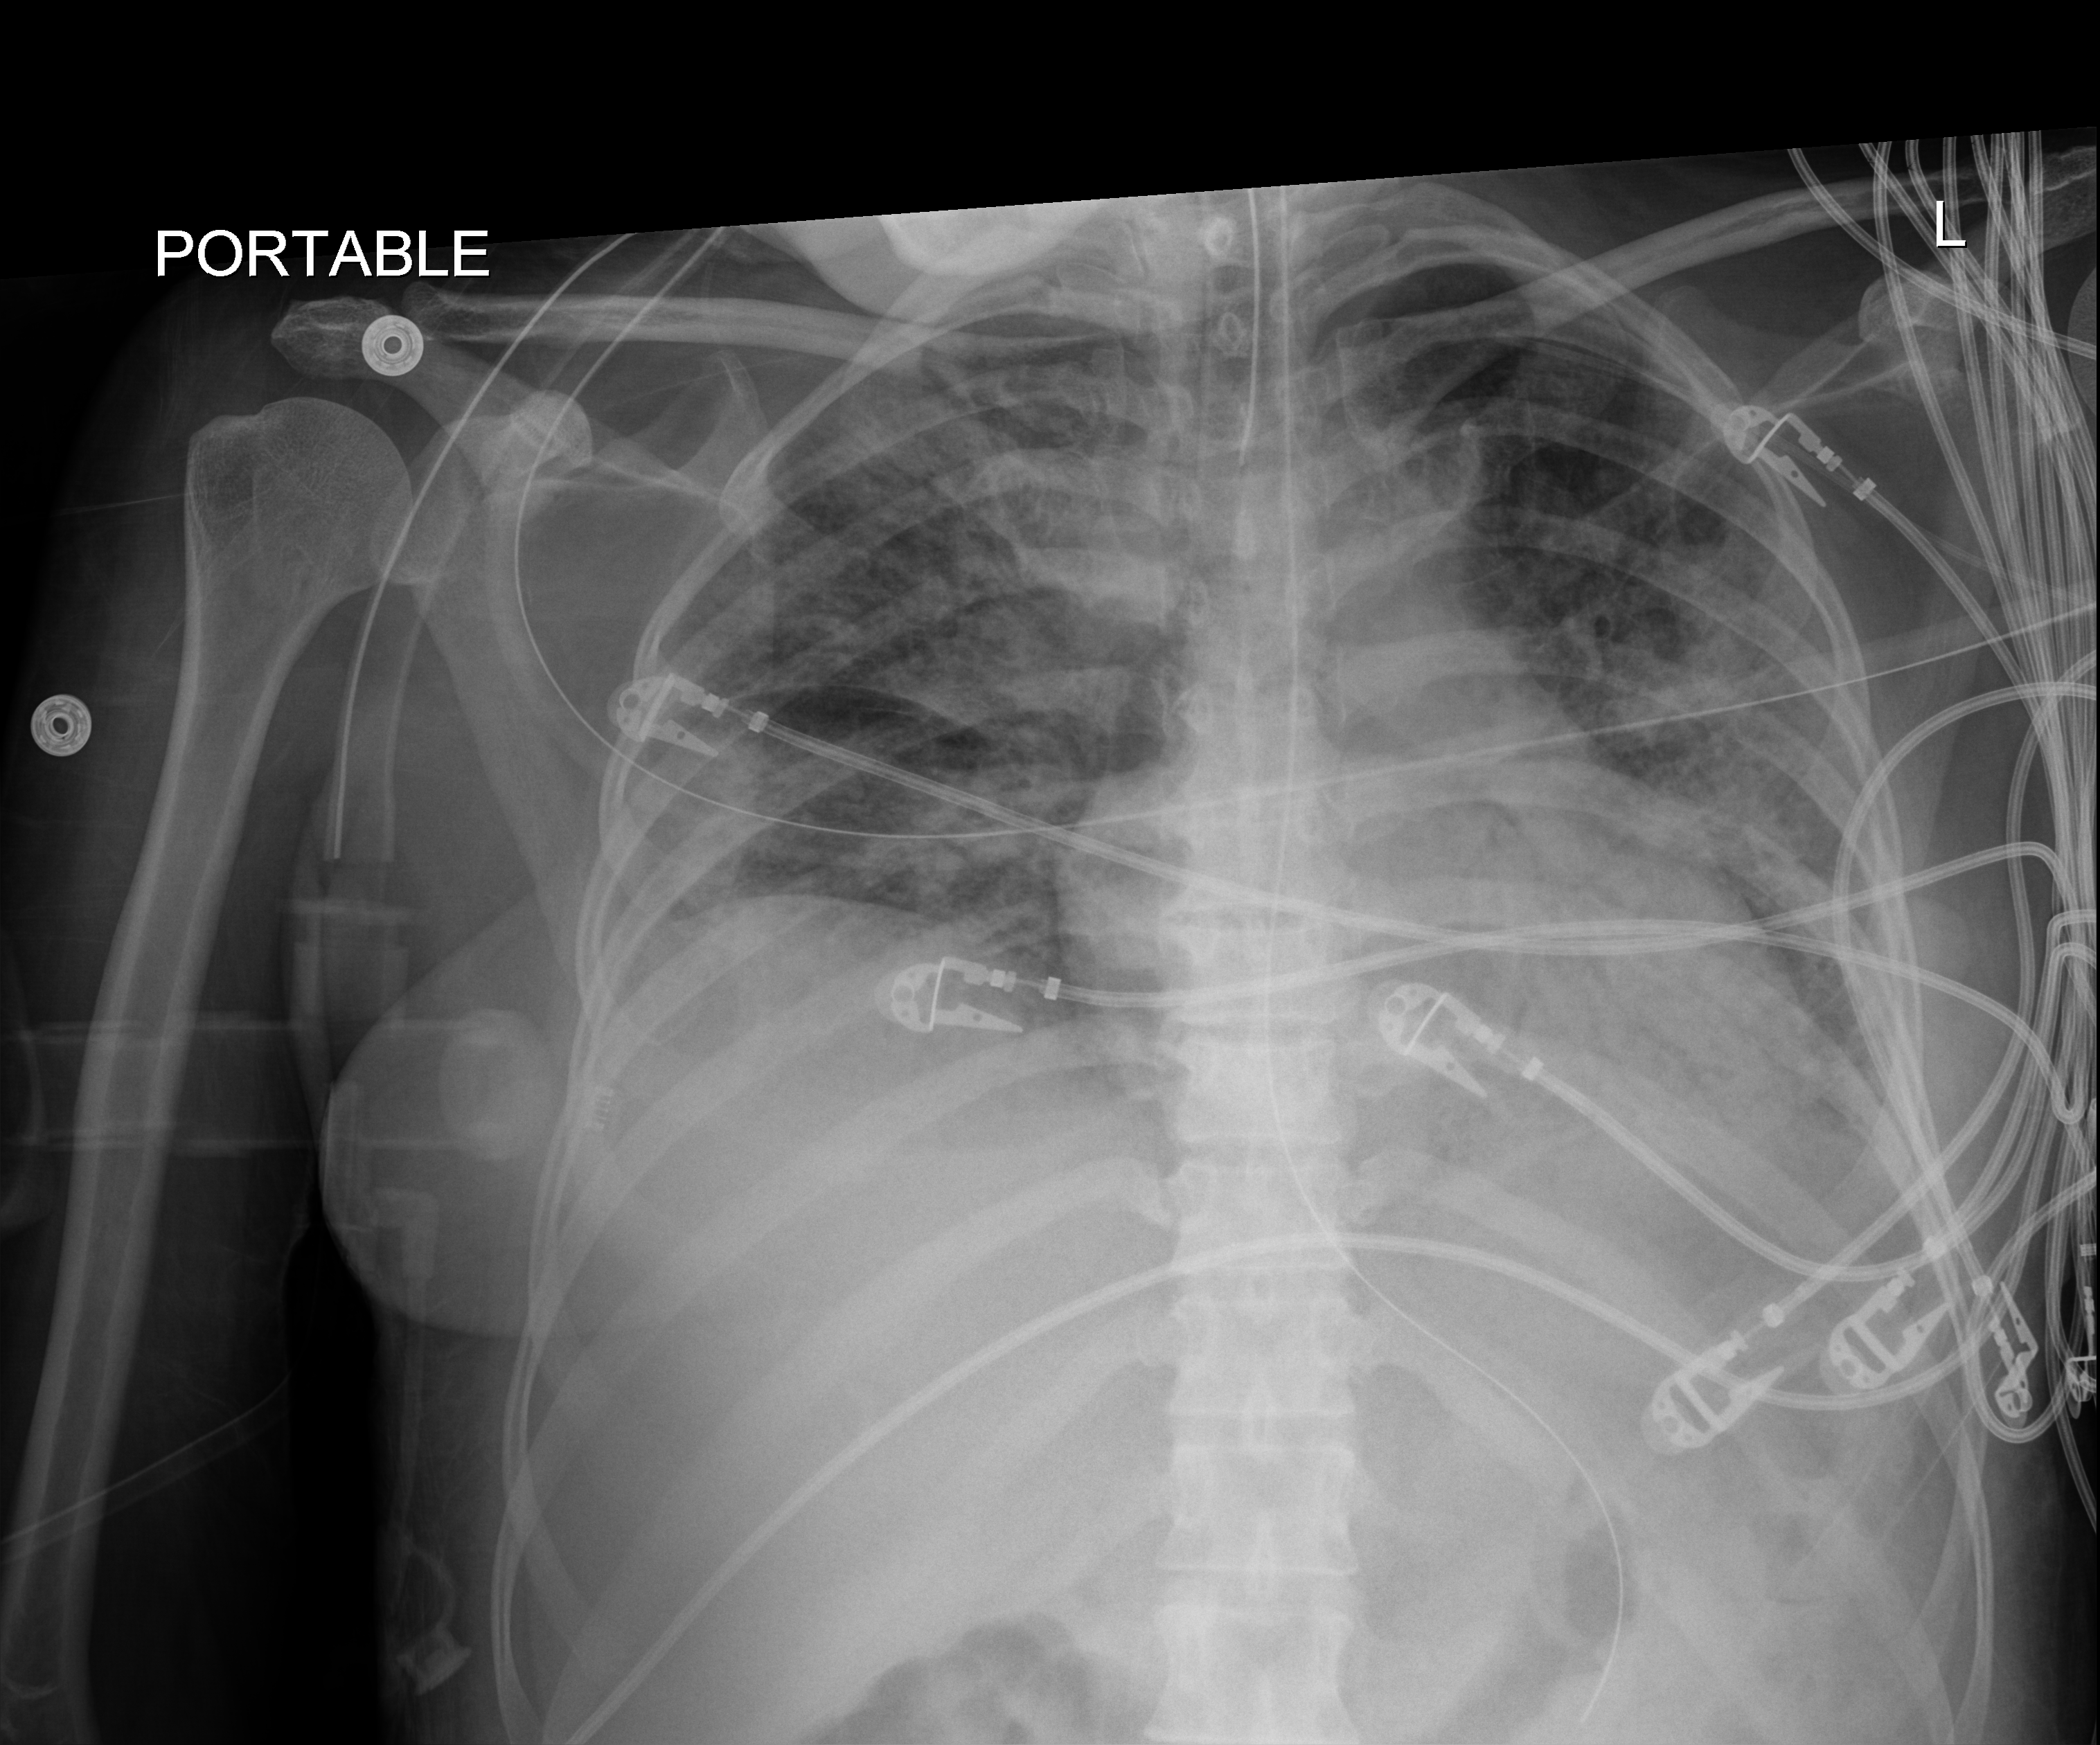
Chest X-ray (portable). Female patient hospitalised with COVID-19, age 18–59 years.
From the hospital-stay record, not from the radiograph (when in the stay this image was taken is not recorded): admitted to intensive care during this hospital stay: yes; mechanically ventilated during this hospital stay: yes; hypertension (admission record): no.